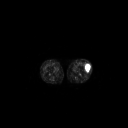
FDG PET of an extremity soft-tissue mass (from a PET/CT study), one axial slice. Slice 172 of 223 in the series (ordered by position). 3.27 mm slice thickness. 128 × 128 image matrix, field of view 700 × 700 mm. Female patient, age 16 years. From the clinical record (not read from this slice): histological type: spindle cell suggestive of biphasic synovial sarcoma; grade: intermediate; site of the primary tumour: left knee.
Structures marked on this image (expert contour drawn on MRI and transferred to this co-registered scan by the dataset authors):
- gross tumour volume including surrounding oedema: box from (x=85, y=63) to (x=90, y=72) px
- gross tumour volume (mass): (x=85, y=63)–(x=90, y=72)